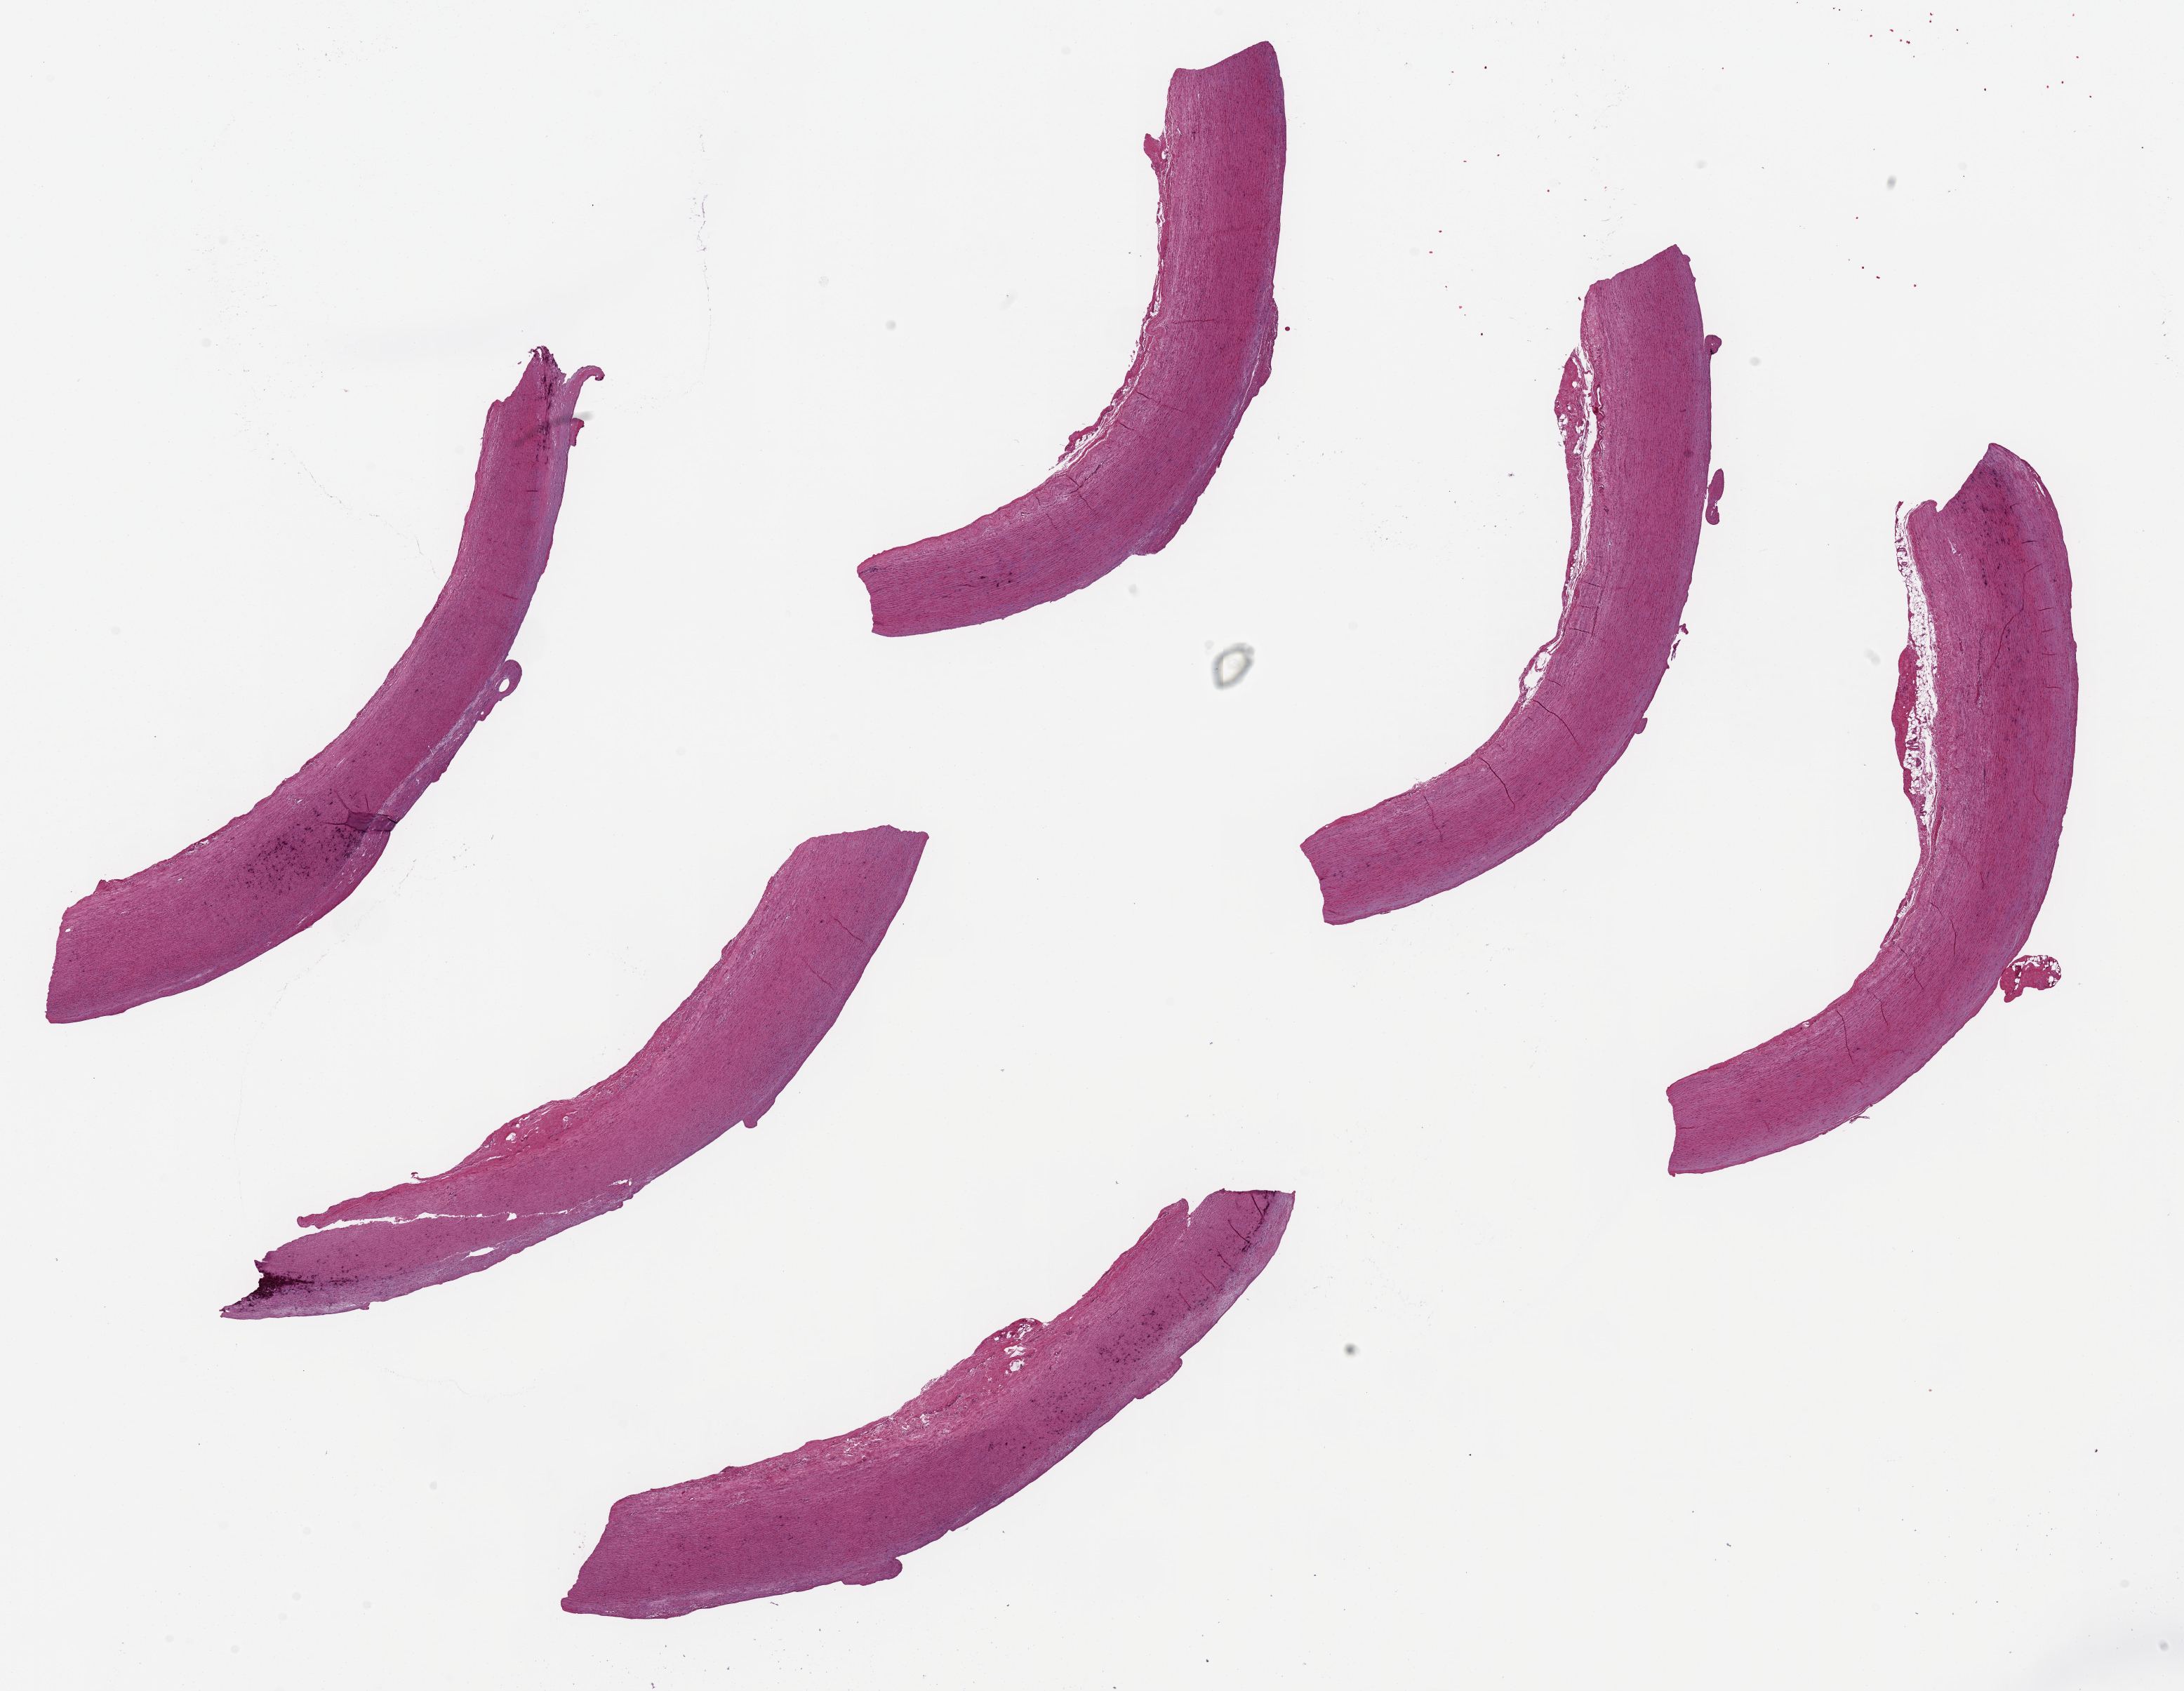
Digitized hematoxylin and eosin (H&E)-stained section, low-resolution overview of the scanned area, about 24.6 x 19.1 mm (from a 20x scan); PAXgene-fixed paraffin-embedded (PFPE) section; section of aorta (target tissue); tissue donor sample.
* review note (as recorded): 6 pieces ~9x1.5mm; no plaques